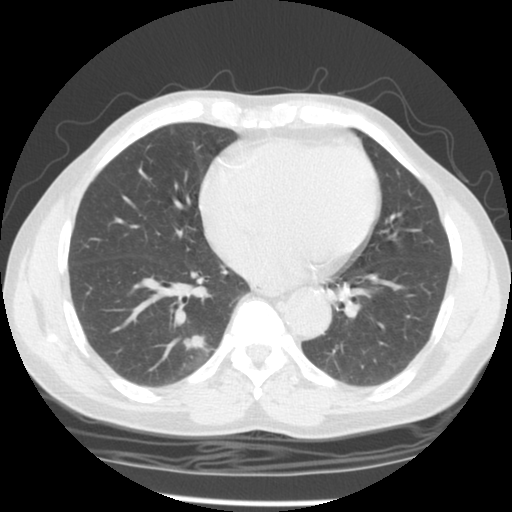
Axial slice from a low-dose chest CT screening exam; third annual screen; lung window (W 1500 / L -600 HU); standard (soft-tissue) reconstruction kernel (STANDARD); slice 55 of 127 in the series. Male participant, aged 58 years at enrolment.
Expert-annotated lung lesion, bounding box (x1, y1, x2, y2) in pixels: (169, 326, 214, 361). The screening reader recorded 2 non-calcified nodules or masses ≥4 mm on this exam (left upper lobe, right lower lobe); which of them this box marks is not recorded. Later outcome: lung cancer diagnosed 323 days after this screen — adenocarcinoma, NOS, right lower lobe, poorly differentiated (G3), stage IIIA (AJCC 6th edition), 15 mm at pathology.